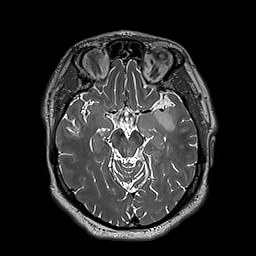
Brain MRI from a brain-tumour surgery series, one axial slice. Position 118 of 192 along the scan axis. 256 × 256 image matrix. From the clinical record (not read from this slice): histopathology: Astrocytoma; WHO grade: 3; IDH mutation: yes; tumour location: Left Insular.
Outlined on this slice (outlined manually by an expert reader):
- tumour: bounding box (x1, y1, x2, y2) in pixels: (153, 105, 176, 131)